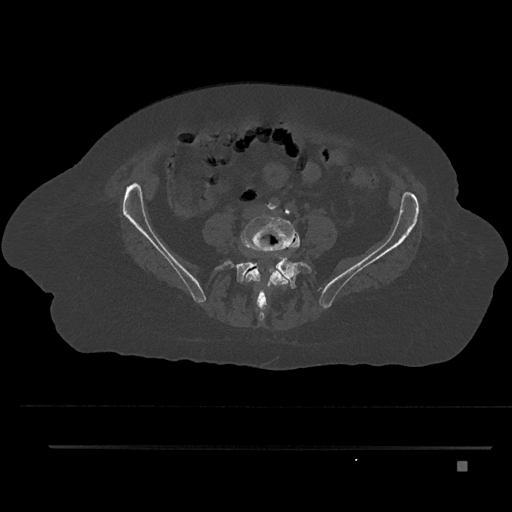
CT including the spine, one axial slice. Position 57 of 797 along the scan axis. 120 kVp. Bone window (W 1800 / L 400 HU). 0.5 mm slice thickness. 512 × 512 image matrix. Patient: female, 76 years. Case-level facts recorded for this patient, not image findings: primary cancer: lung.
Outlined on this slice (semi-automatically segmented with operator editing):
- L4 vertebra: bounding box (x1, y1, x2, y2) in pixels: (242, 216, 300, 314)
- L5 vertebra: (215, 241, 312, 321)